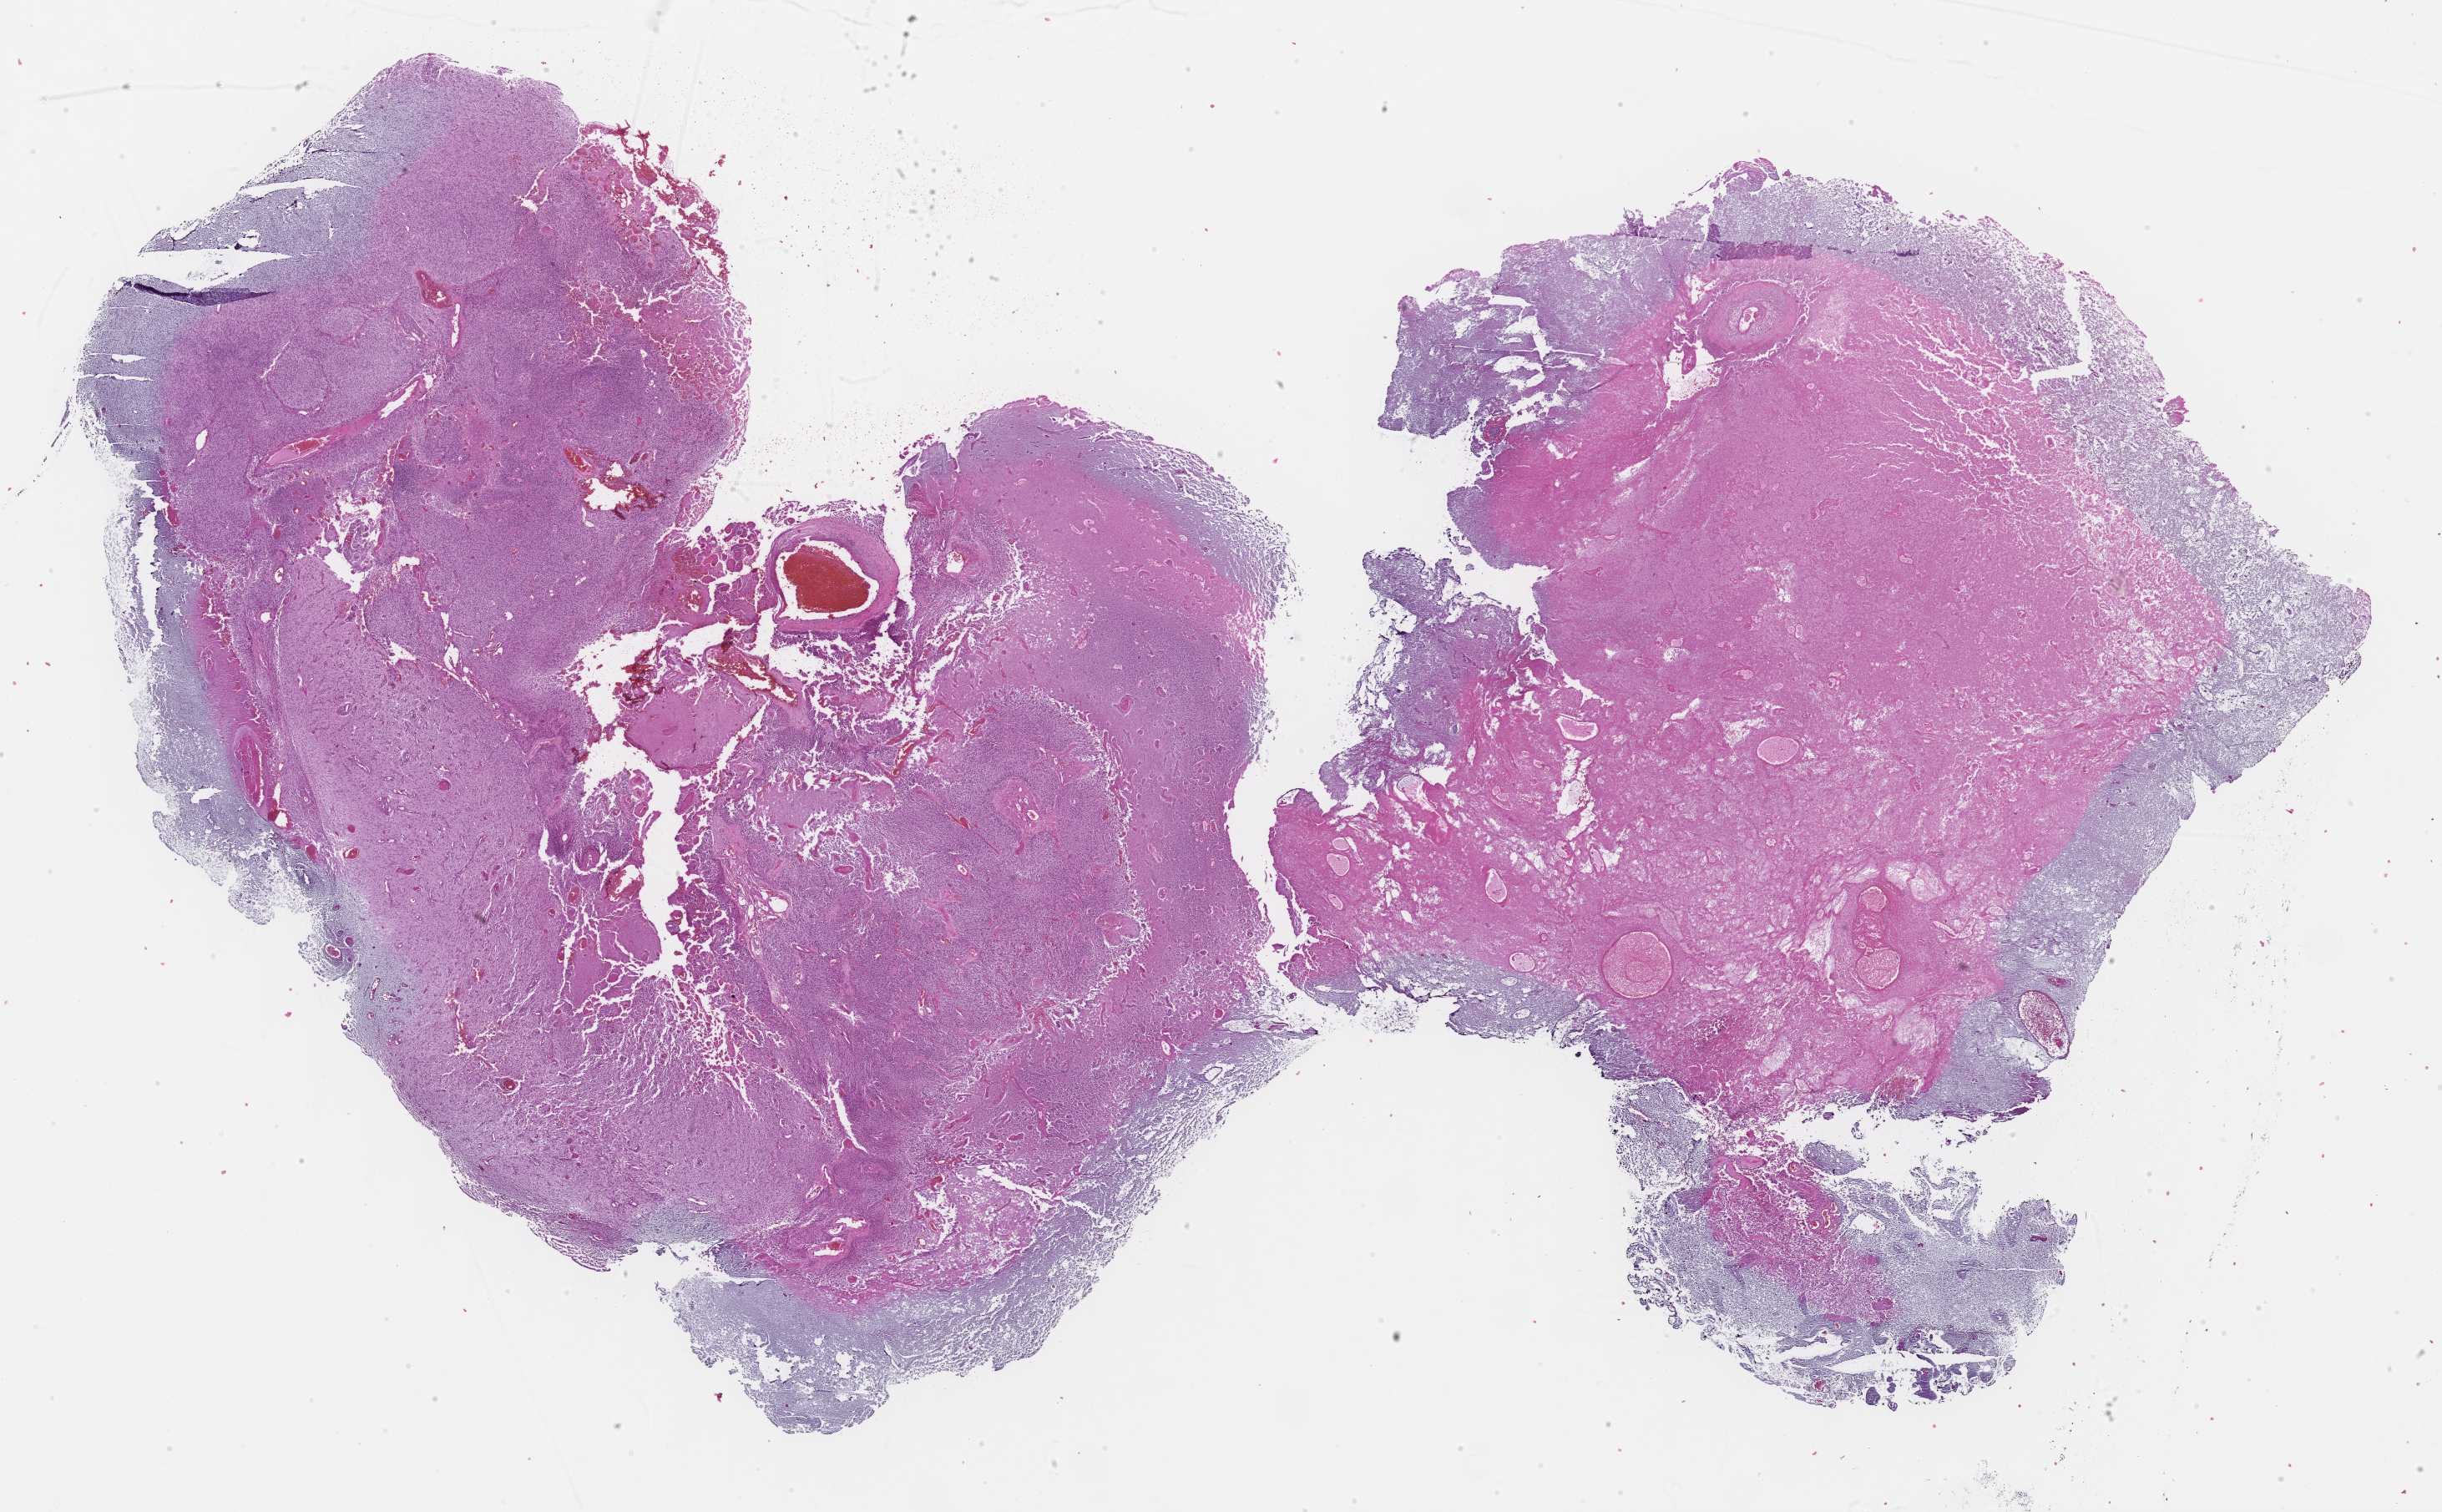
H&E-stained whole-slide image, low-resolution overview of the scanned area, about 23.7 x 14.7 mm (slide scanned at 40x), formalin-fixed paraffin-embedded (FFPE) diagnostic section, primary tumour sample from the brain. Female, age 77 years at initial diagnosis.
Diagnosis: Glioblastoma.